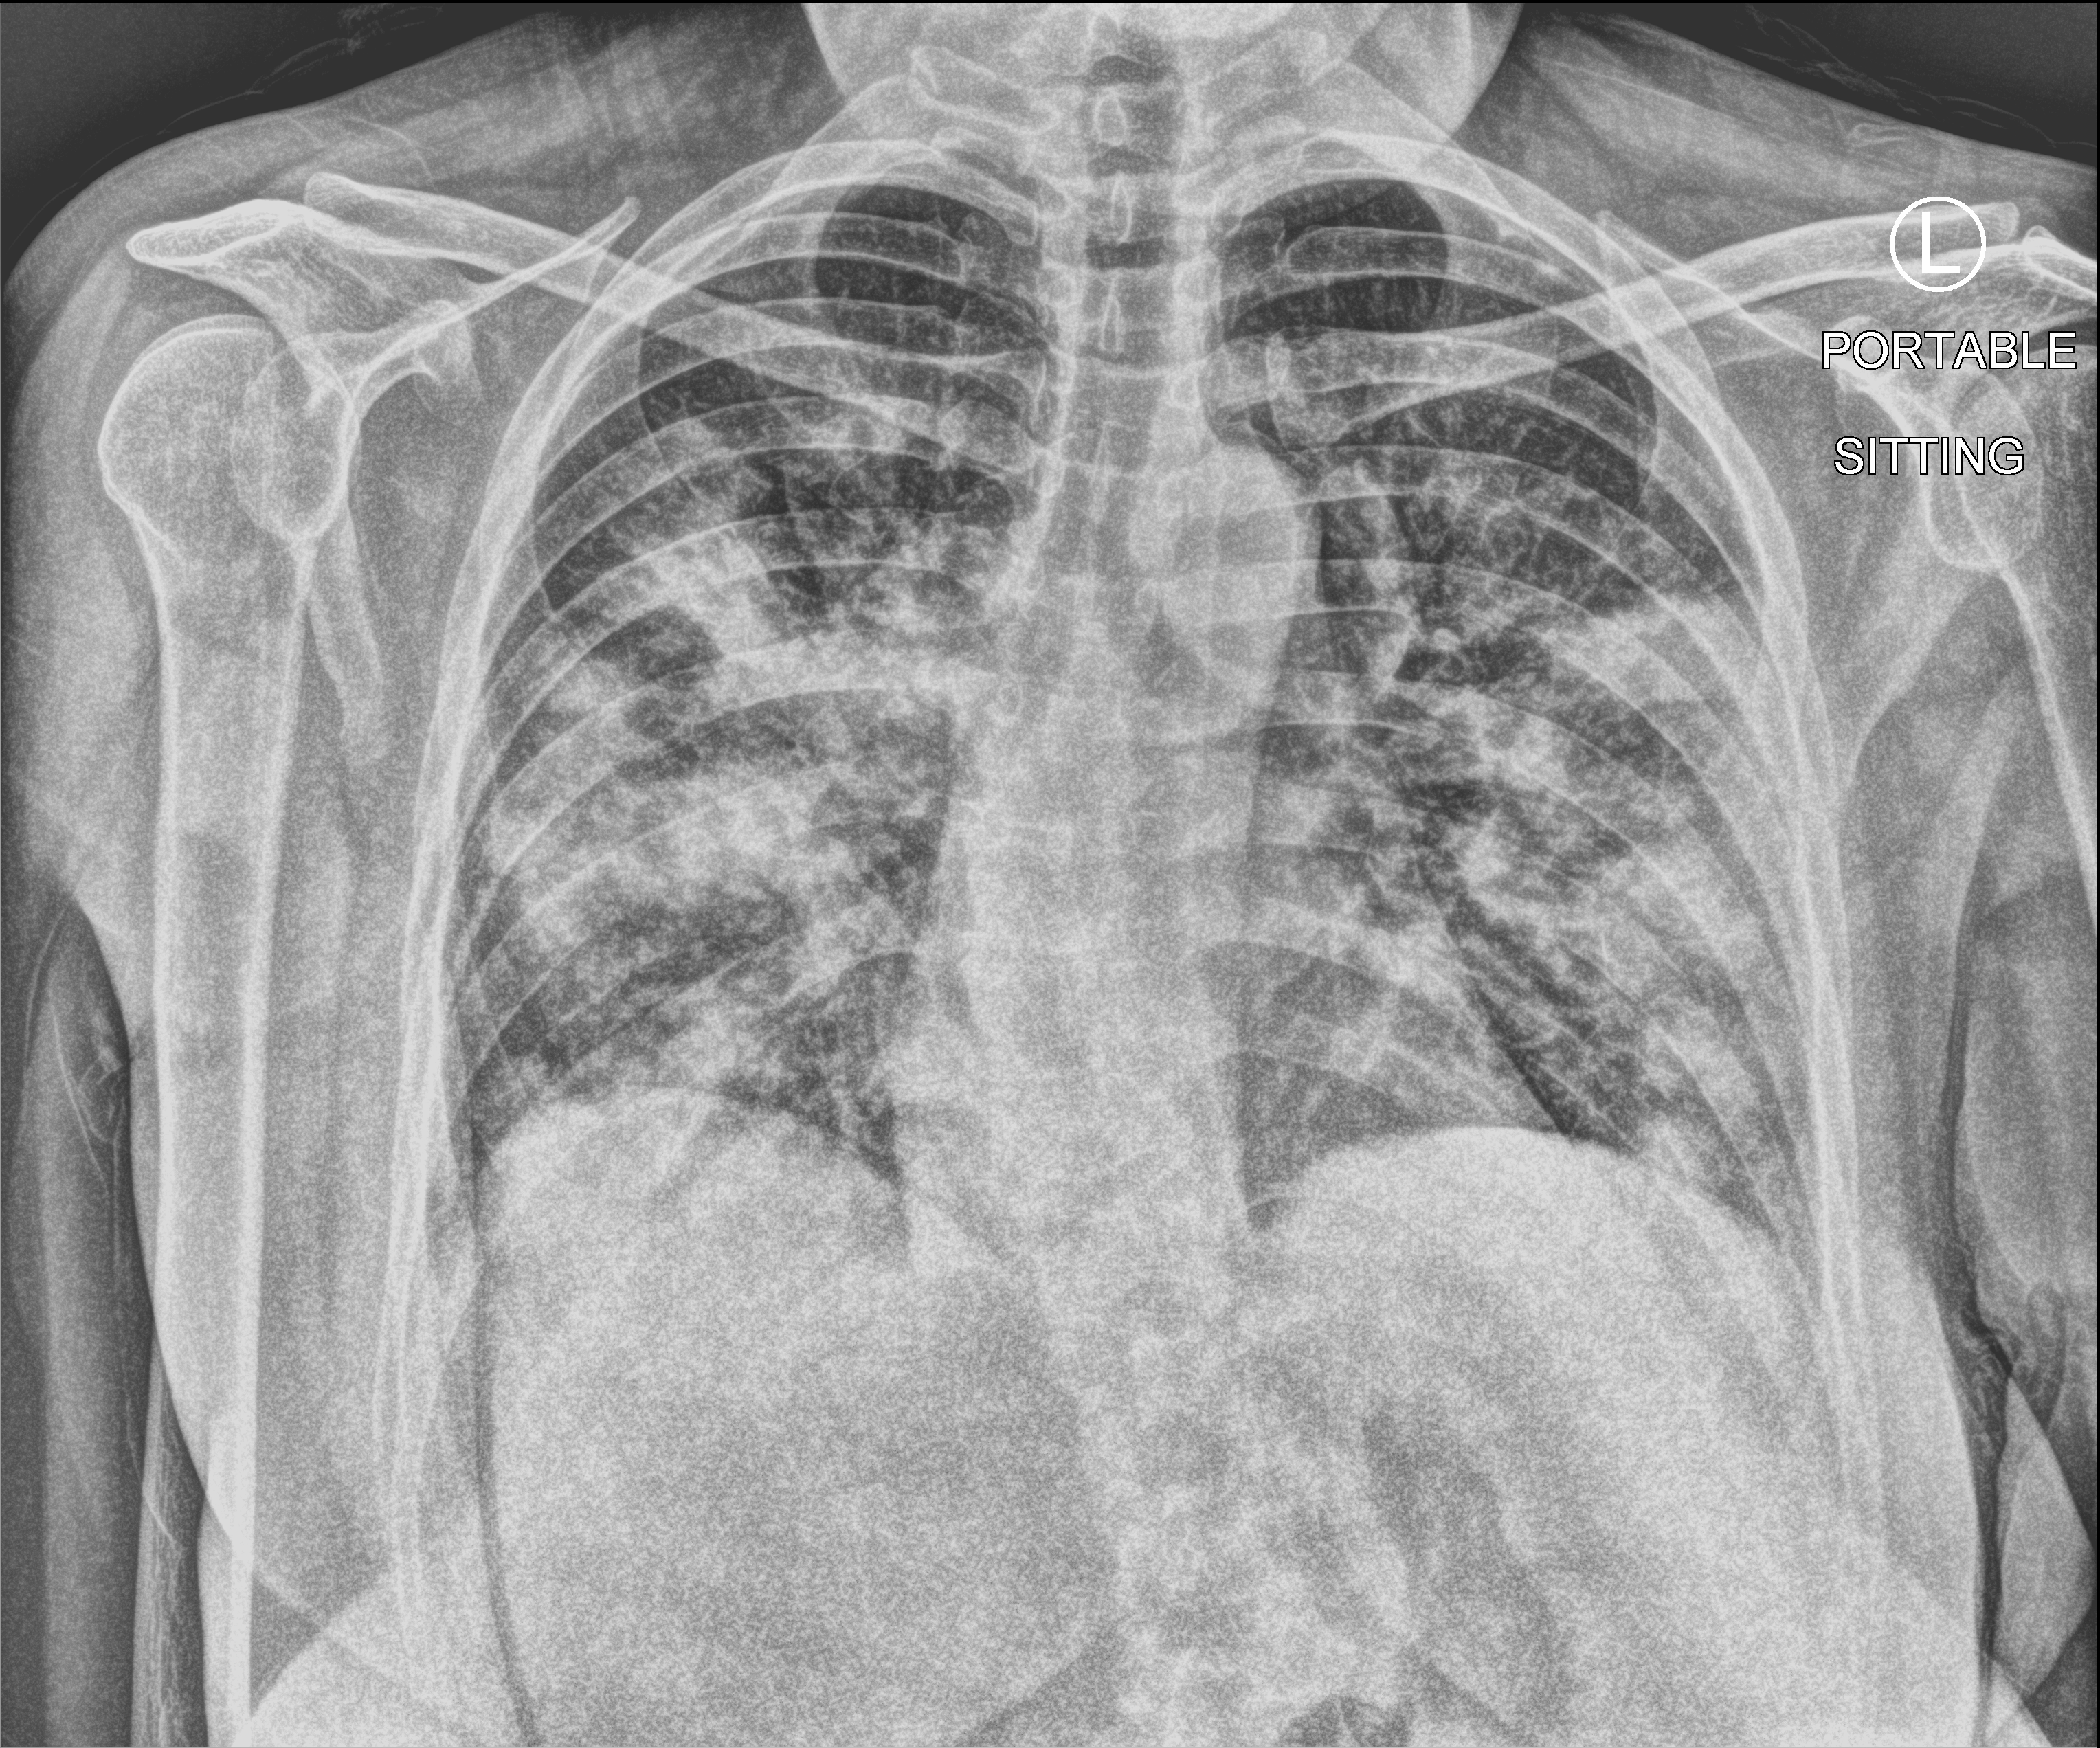
Portable chest radiograph, anteroposterior (AP) projection. Patient hospitalised with COVID-19; female, aged 18–59 years.
Hospital-stay facts (about this admission, not read from this image; timing relative to this image not recorded): length of hospital stay: 3 days; COPD (admission record): no; smoking status (admission record): never.